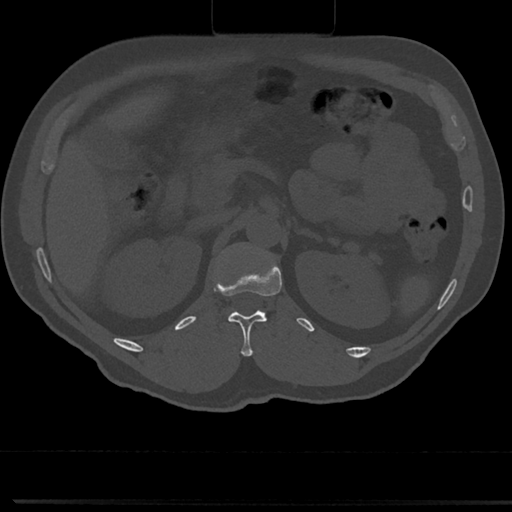
CT including the spine, one axial slice. Position 126 of 817 along the scan axis. Bone window (W 1800 / L 400 HU). 512 × 512 image matrix, field of view 355 × 355 mm. Male patient, age 61 years. From the clinical record (not read from this slice): primary cancer: prostate.
Outlined on this slice (semi-automatically segmented with operator editing):
- L1 vertebra: box from (x=212, y=241) to (x=273, y=319) px
- T12 vertebra: (x=226, y=281)–(x=281, y=356)